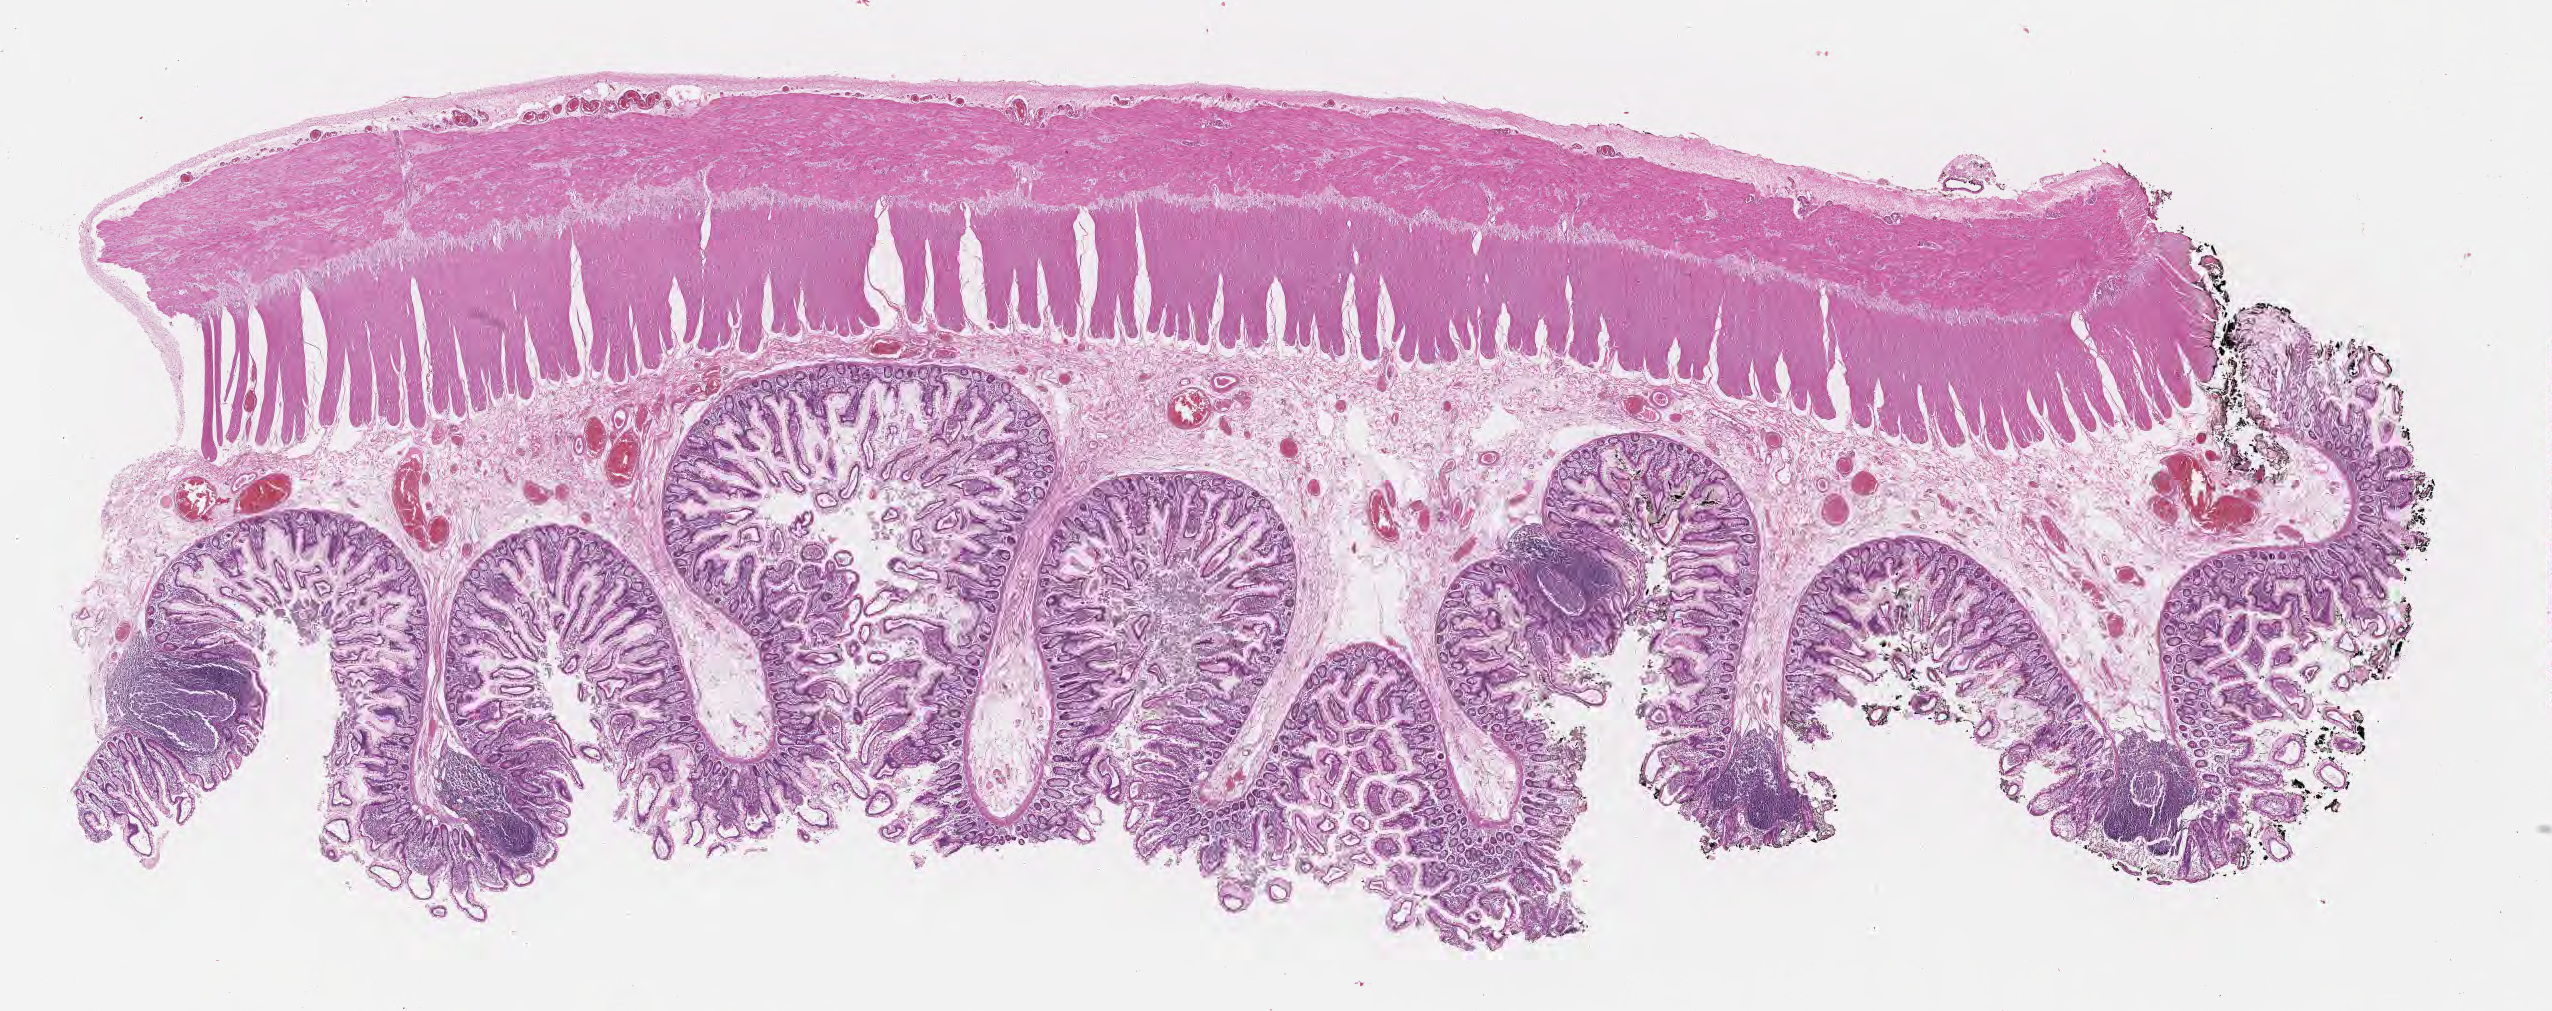
Whole-slide image, H&E stain, low-resolution overview of the scanned area, about 20.6 x 8.2 mm. FFPE section. Specimen: non-tumor (normal tissue) sample from a patient with burkitt lymphoma, NOS. Patient: female, age at initial diagnosis 8 years. Pathologist review of this section (percent, as recorded): tumor cells 0%, tumor nuclei 0%.
This section: non-tumor tissue sample; the patient's diagnosis is given above.